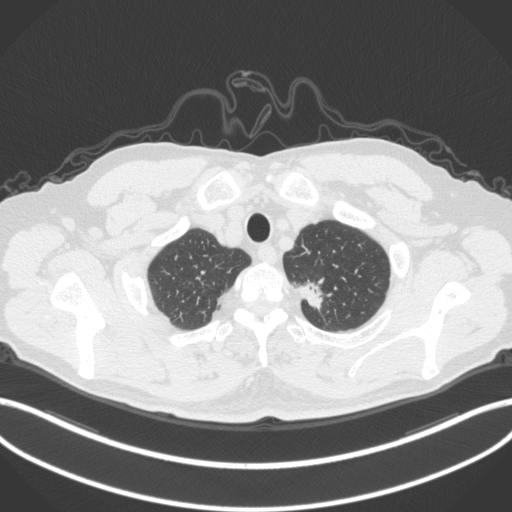
Chest CT, one axial slice; slice 341 of 382 in the series (ordered by position); reconstruction kernel B31f; lung window (W 1500 / L -600 HU); 1 mm slice thickness; 512 × 512 image matrix, field of view 400 × 400 mm. Male patient, age 64 years. From the clinical record (not read from this slice): clinical TNM (as recorded): T1c N0 M0.
Outlined on this slice (bounding box drawn by a radiologist):
- lung tumour (recorded histology: adenocarcinoma): box from (x=294, y=276) to (x=333, y=314) px